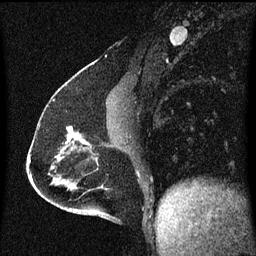
Breast MRI (dynamic contrast-enhanced), one sagittal slice; slice 27 of 60 in the series (ordered by position); dynamic contrast-enhanced series, image 2 of 3 at this slice position (ordered by acquisition); 1.5 T; TE 4.2 ms, TR 8 ms; 2 mm slice thickness; 256 × 256 image matrix. Female patient, age 51 years.
Annotated regions visible in this slice (semi-automatically segmented with operator editing):
- analysis volume of interest (the breast-tissue region the enhancement analysis was run in; not a lesion): bounding box (x1, y1, x2, y2) in pixels: (62, 126, 93, 149)
- tumour enhancement mask (voxels above the 70 % enhancement threshold inside the analysis volume of interest): (66, 126, 89, 145)